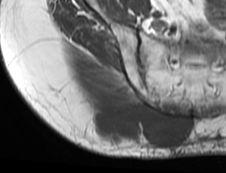
MRI of an extremity soft-tissue mass, one axial slice; slice 50 of 73 in the series (ordered by position); MR volume resampled by the dataset authors to the PET/CT grid (not the native acquisition matrix); 3.27 mm slice thickness; 226 × 173 image matrix. Female patient. Case-level facts recorded for this patient, not image findings: histological type: spindle cell suggestive of myxofibrosarcoma; grade: intermediate; site of the primary tumour: right buttock.
Structures marked on this image (expert contour drawn on MRI and transferred to this co-registered scan by the dataset authors):
- gross tumour volume (mass): bounding box (x1, y1, x2, y2) in pixels: (86, 101, 190, 150)